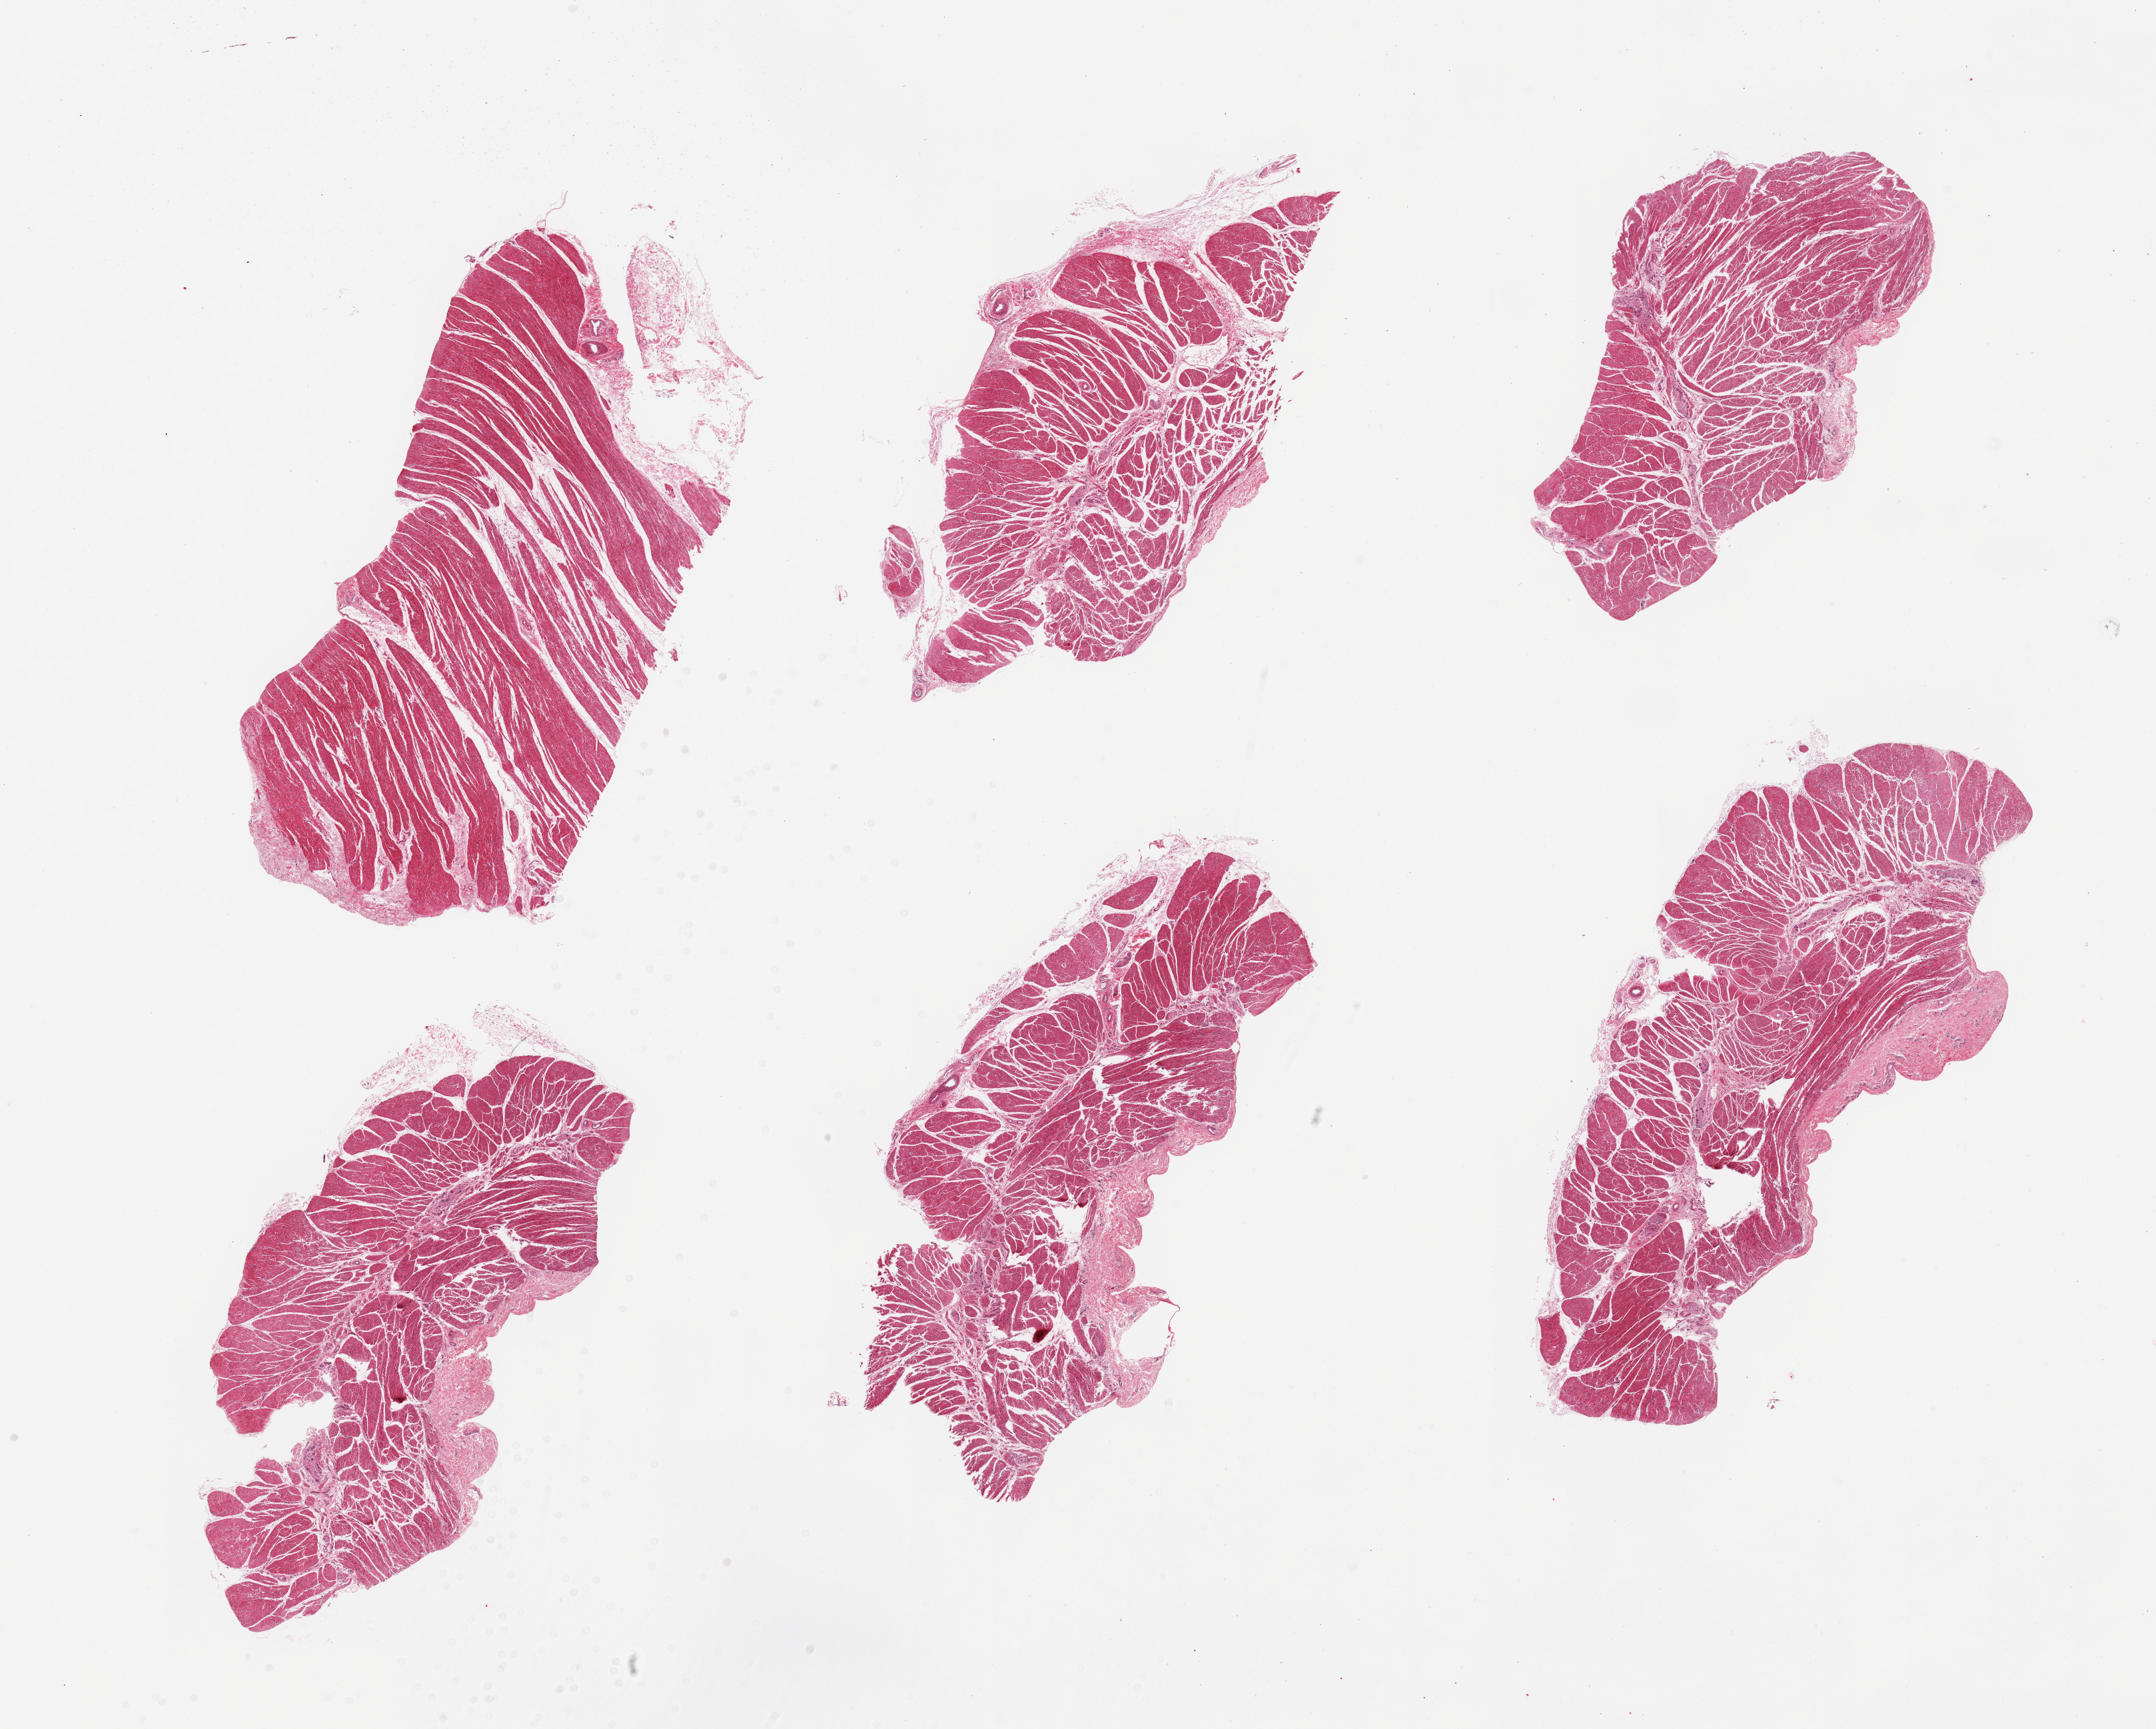
Digitized H&E-stained section — a low-resolution overview of the entire scanned area, about 25.6 x 20.5 mm, PAXgene-fixed, paraffin-embedded tissue, section of esophageal muscle (target tissue), tissue donor sample. Female donor.
Review note (as recorded): 6 pieces, confirmed target muscularis.